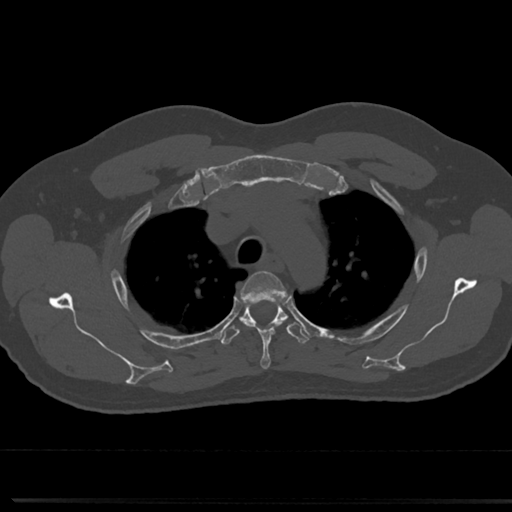
CT including the spine, one axial slice; reconstruction kernel Br40s/3; bone window (W 1800 / L 400 HU); 512 × 512 image matrix, field of view 355 × 355 mm. Patient: male, 61 years. Case-level facts recorded for this patient, not image findings: primary cancer: prostate.
Structures marked on this image (semi-automatically segmented with operator editing):
- T3 vertebra: box from (x=241, y=270) to (x=284, y=369) px
- T4 vertebra: (x=219, y=300)–(x=310, y=345)